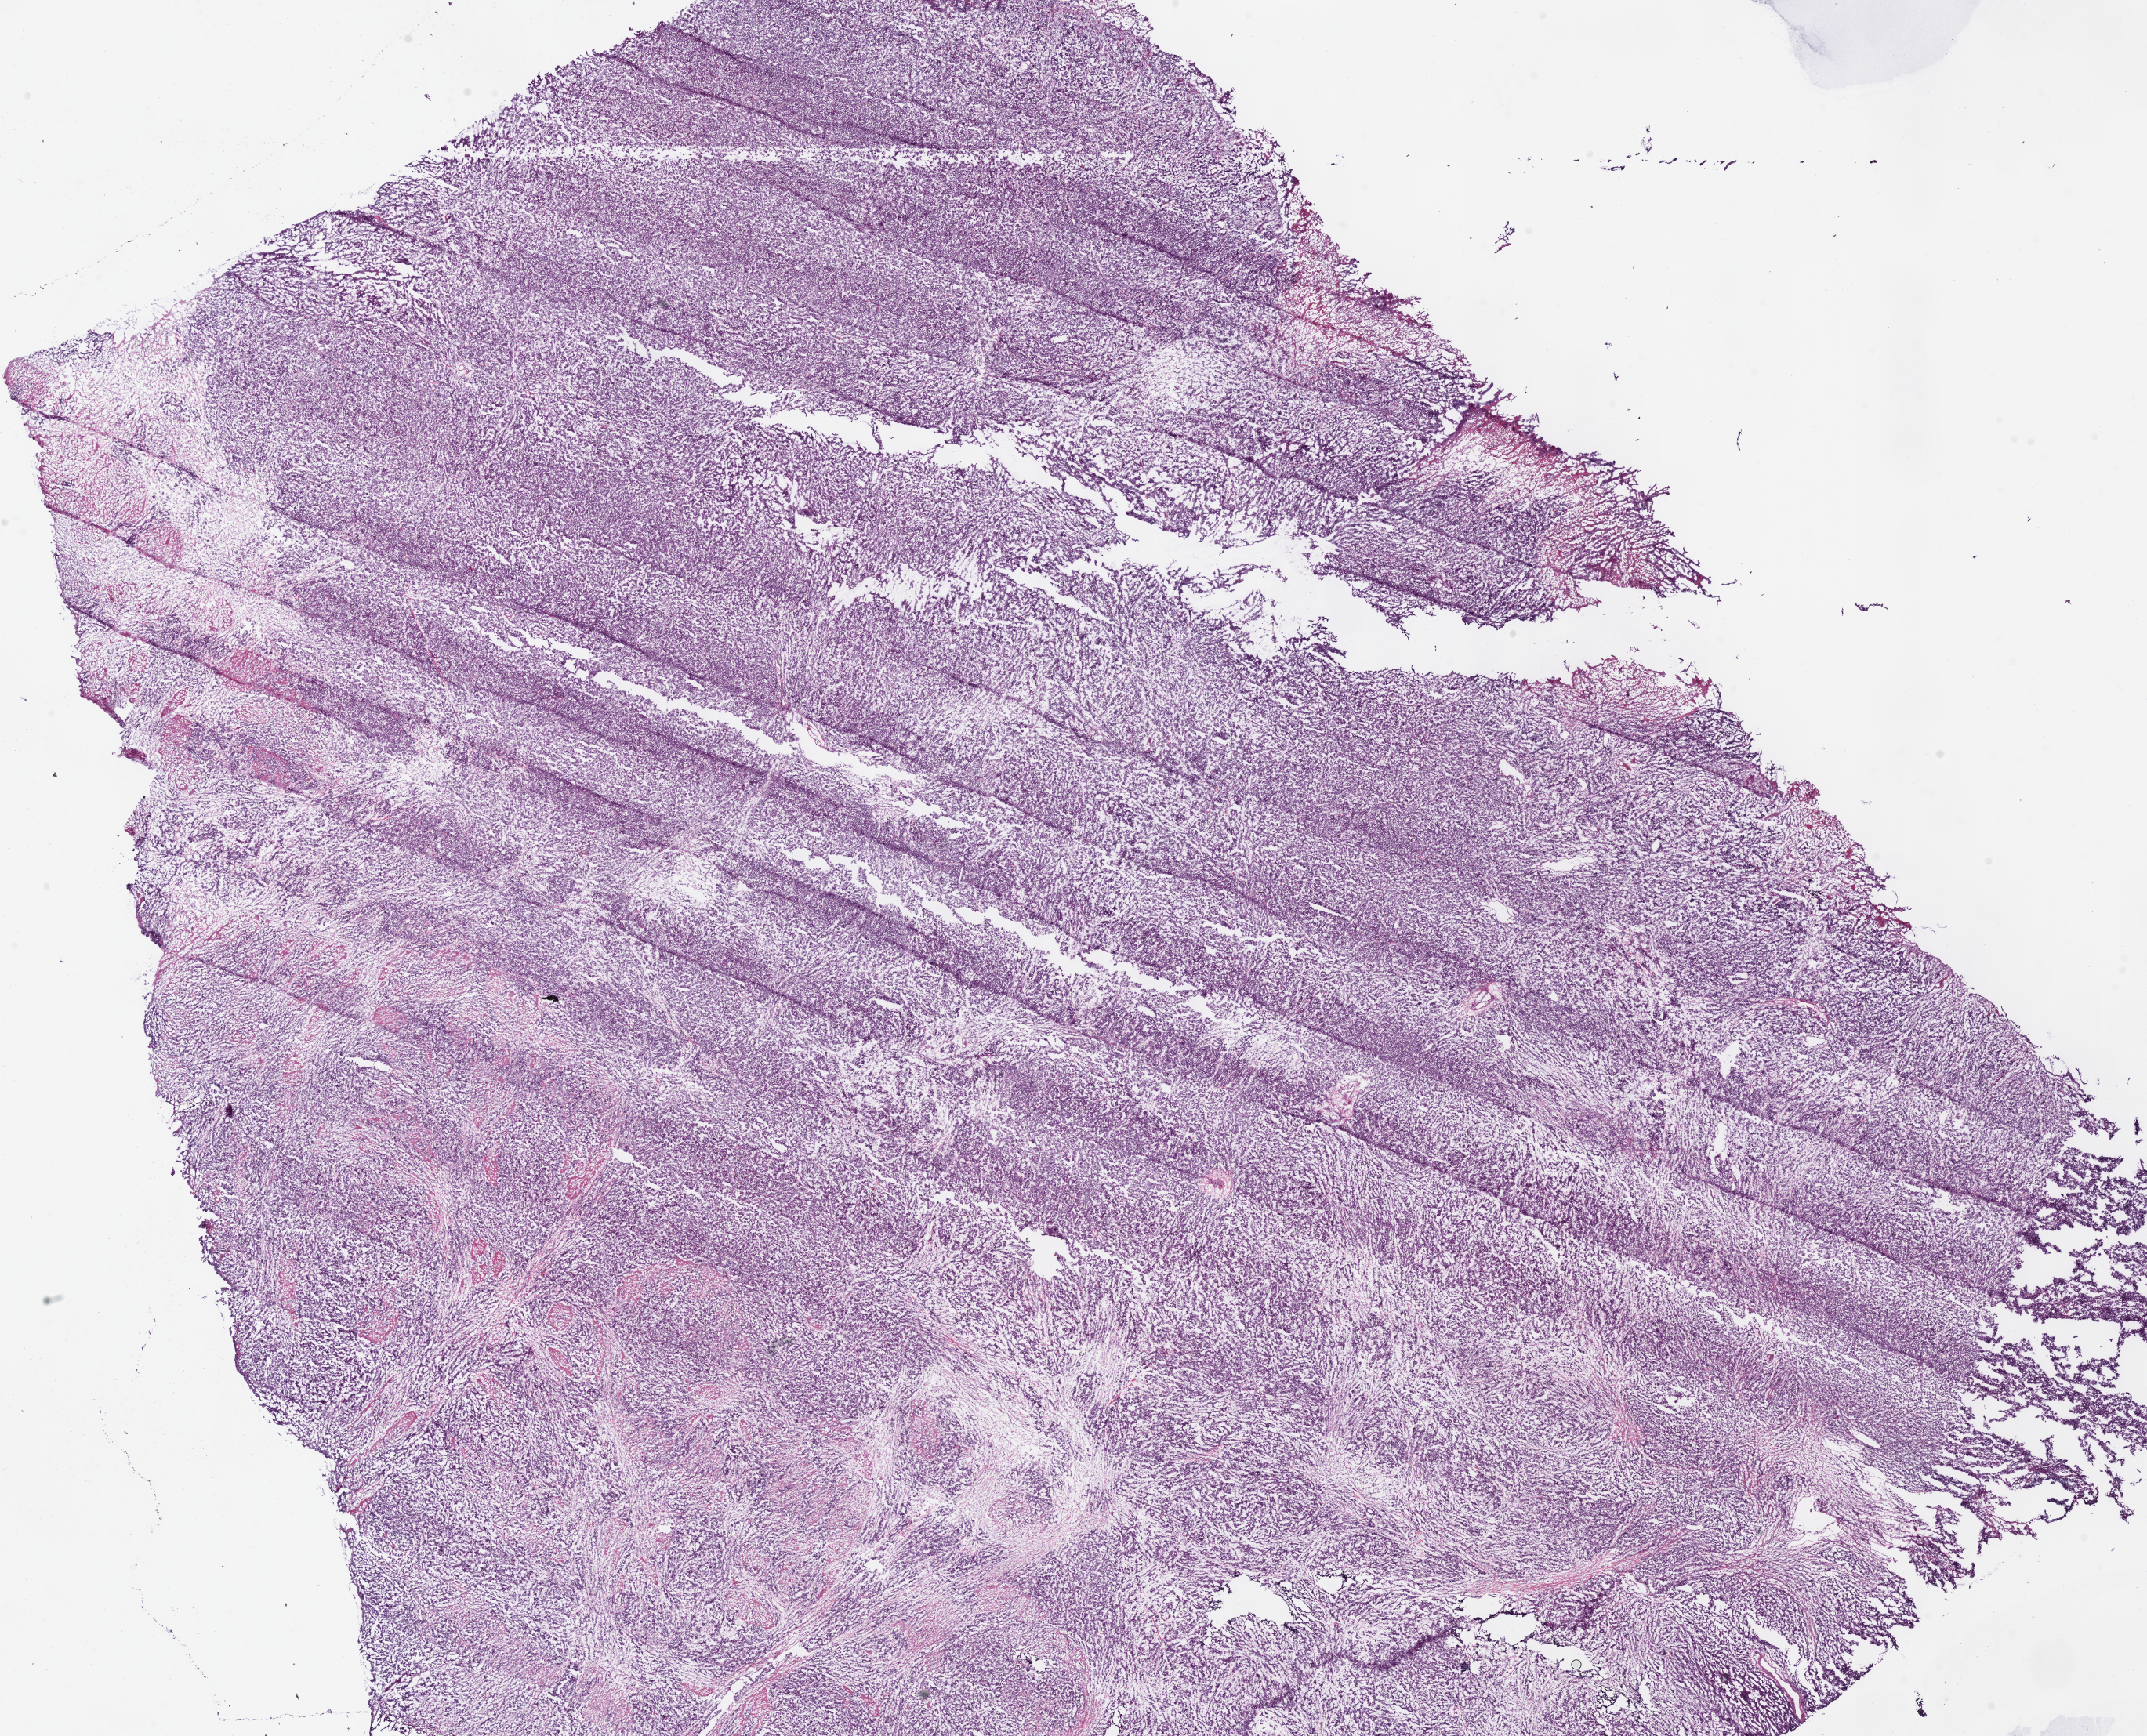
H&E-stained whole-slide image — a low-resolution overview of the entire scanned area, about 21.5 x 17.4 mm (from a 40x scan); frozen section from the bottom of the tissue portion; primary tumour sample from the stomach. Female patient; age at initial diagnosis 71 years. Histologic grade: G3 (poorly differentiated). Slide review estimates, as recorded: tumour cells 85%, tumour nuclei 75%, normal cells 0%, stromal cells 15%, necrosis 0%.
AJCC pathologic stage: IIIC. Diagnosis: Adenocarcinoma, NOS. Lymph nodes positive (case pathology): 6 of 10 examined.